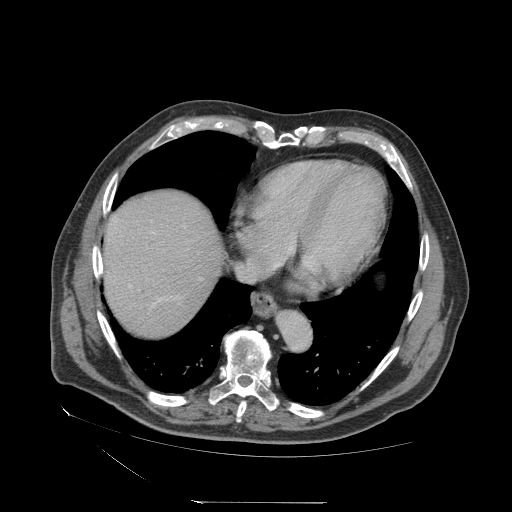
Contrast-enhanced abdominal CT (liver protocol), one axial slice. Slice 66 of 83 in the series (ordered by position). Reconstruction kernel STANDARD. Soft-tissue window (W 400 / L 40 HU). 2.5 mm slice thickness. 512 × 512 image matrix, field of view 460 × 460 mm. From the clinical record (not read from this slice): diagnosis: hepatocellular carcinoma (patient treated with transarterial chemoembolisation; whether this scan precedes or follows treatment is not stated here); TNM stage (as recorded): Stage-I; Child-Pugh class: A; tumour differentiation: well differentiated.
Annotated regions visible in this slice (semi-automatic segmentation, software-assisted and operator-edited):
- abdominal aorta: bounding box (x1, y1, x2, y2) in pixels: (277, 311, 311, 349)
- liver parenchyma outside the tumour (the mass and vessels are separate outlines, so this box may not span the whole liver): (102, 190, 222, 336)
- liver vessels: (129, 232, 163, 305)